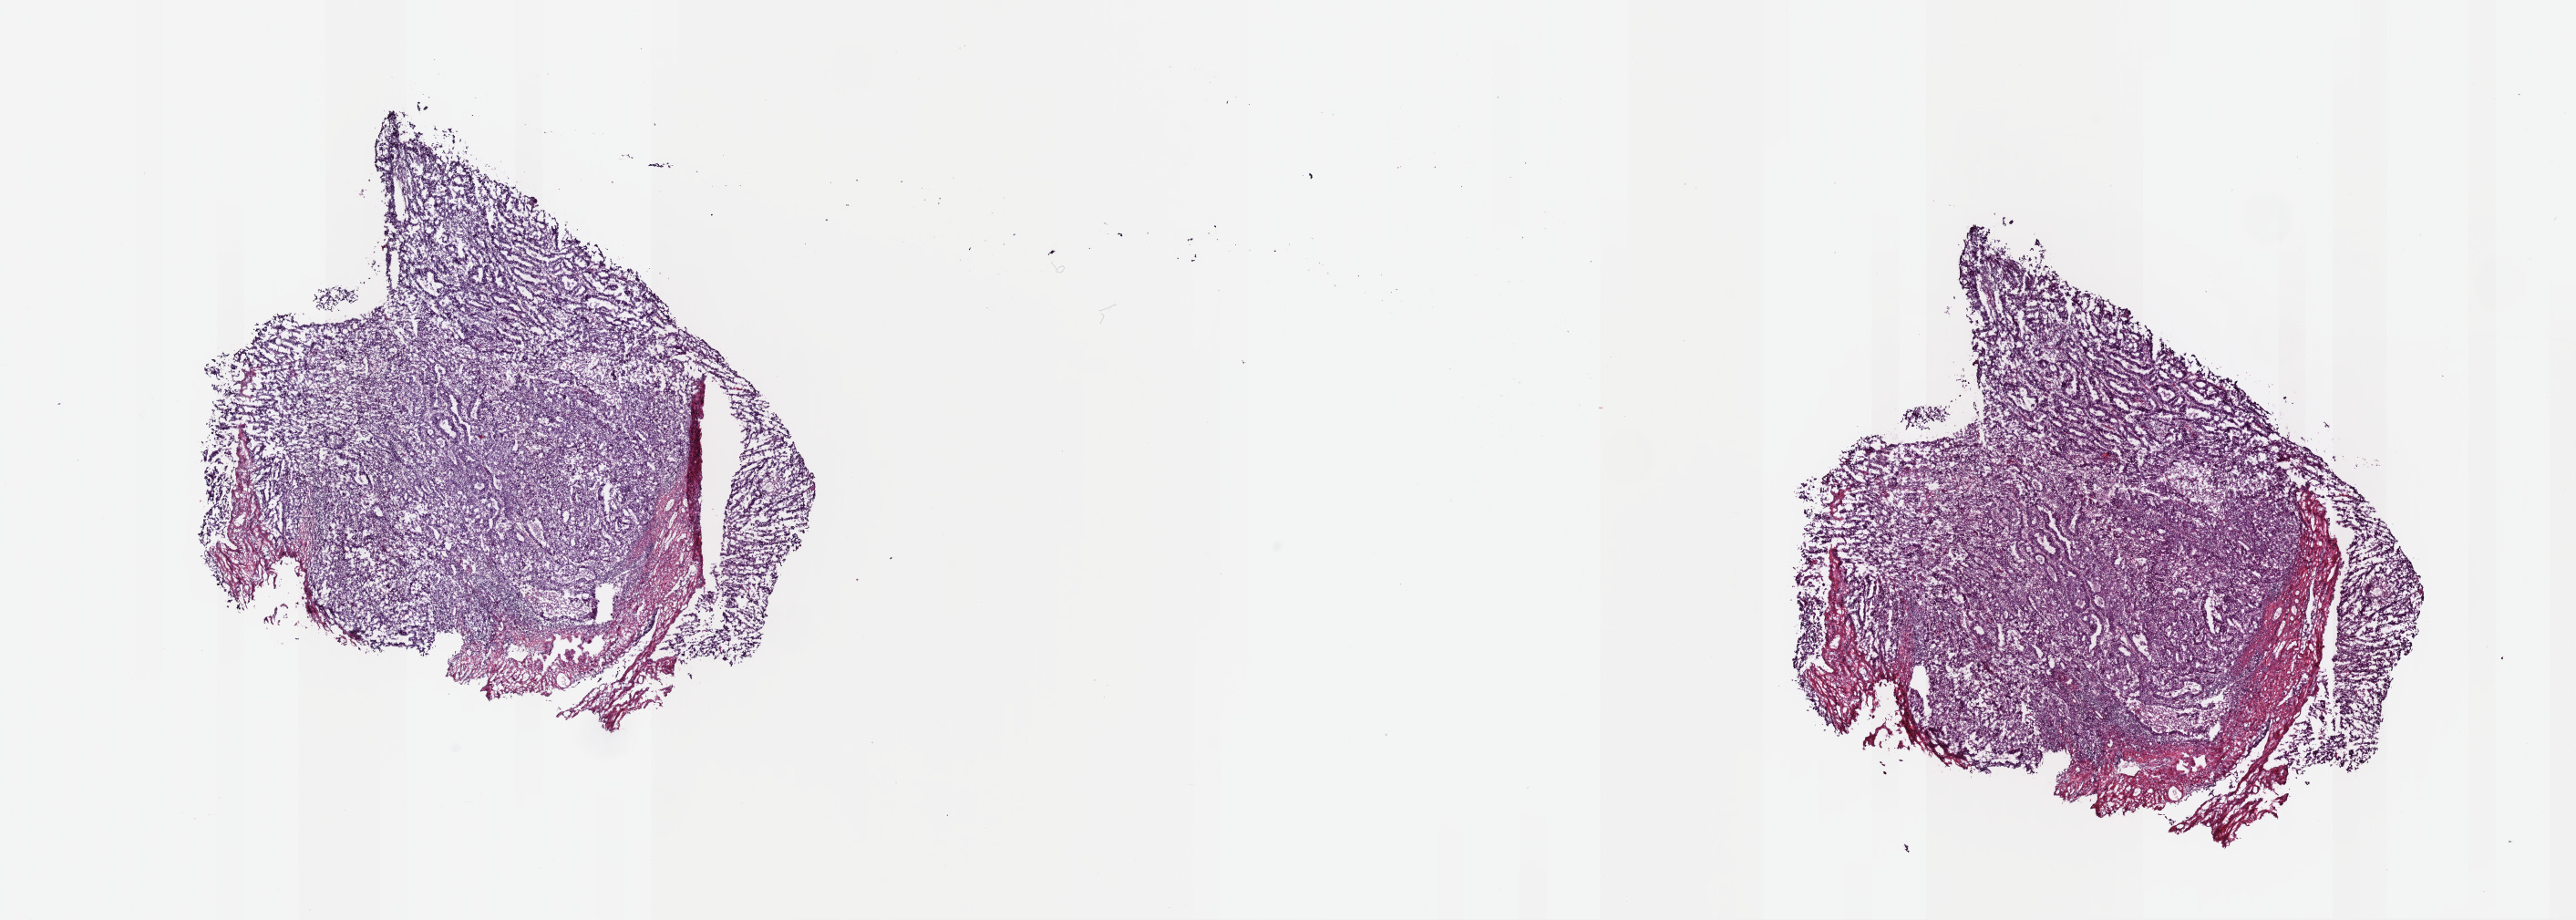
Digitized H&E tissue section (whole slide) — whole scanned area (about 22.3 x 8.0 mm, slide scanned at 40x) shown as a low-resolution overview. Frozen section. Primary tumour sample from the uterus. Female, age 68 years at initial diagnosis. Histologic grade: G3 (poorly differentiated). Pathologist review of this section (percent, as recorded): tumour cells 85%, tumour nuclei 90%, normal cells 10%, stromal cells 0%, necrosis 5%. Inflammatory infiltration, as recorded: lymphocyte infiltration 2%, monocyte infiltration 1%, neutrophil infiltration 0%.
- diagnosis: Endometrioid adenocarcinoma, NOS (endometrium)
- FIGO stage: IC